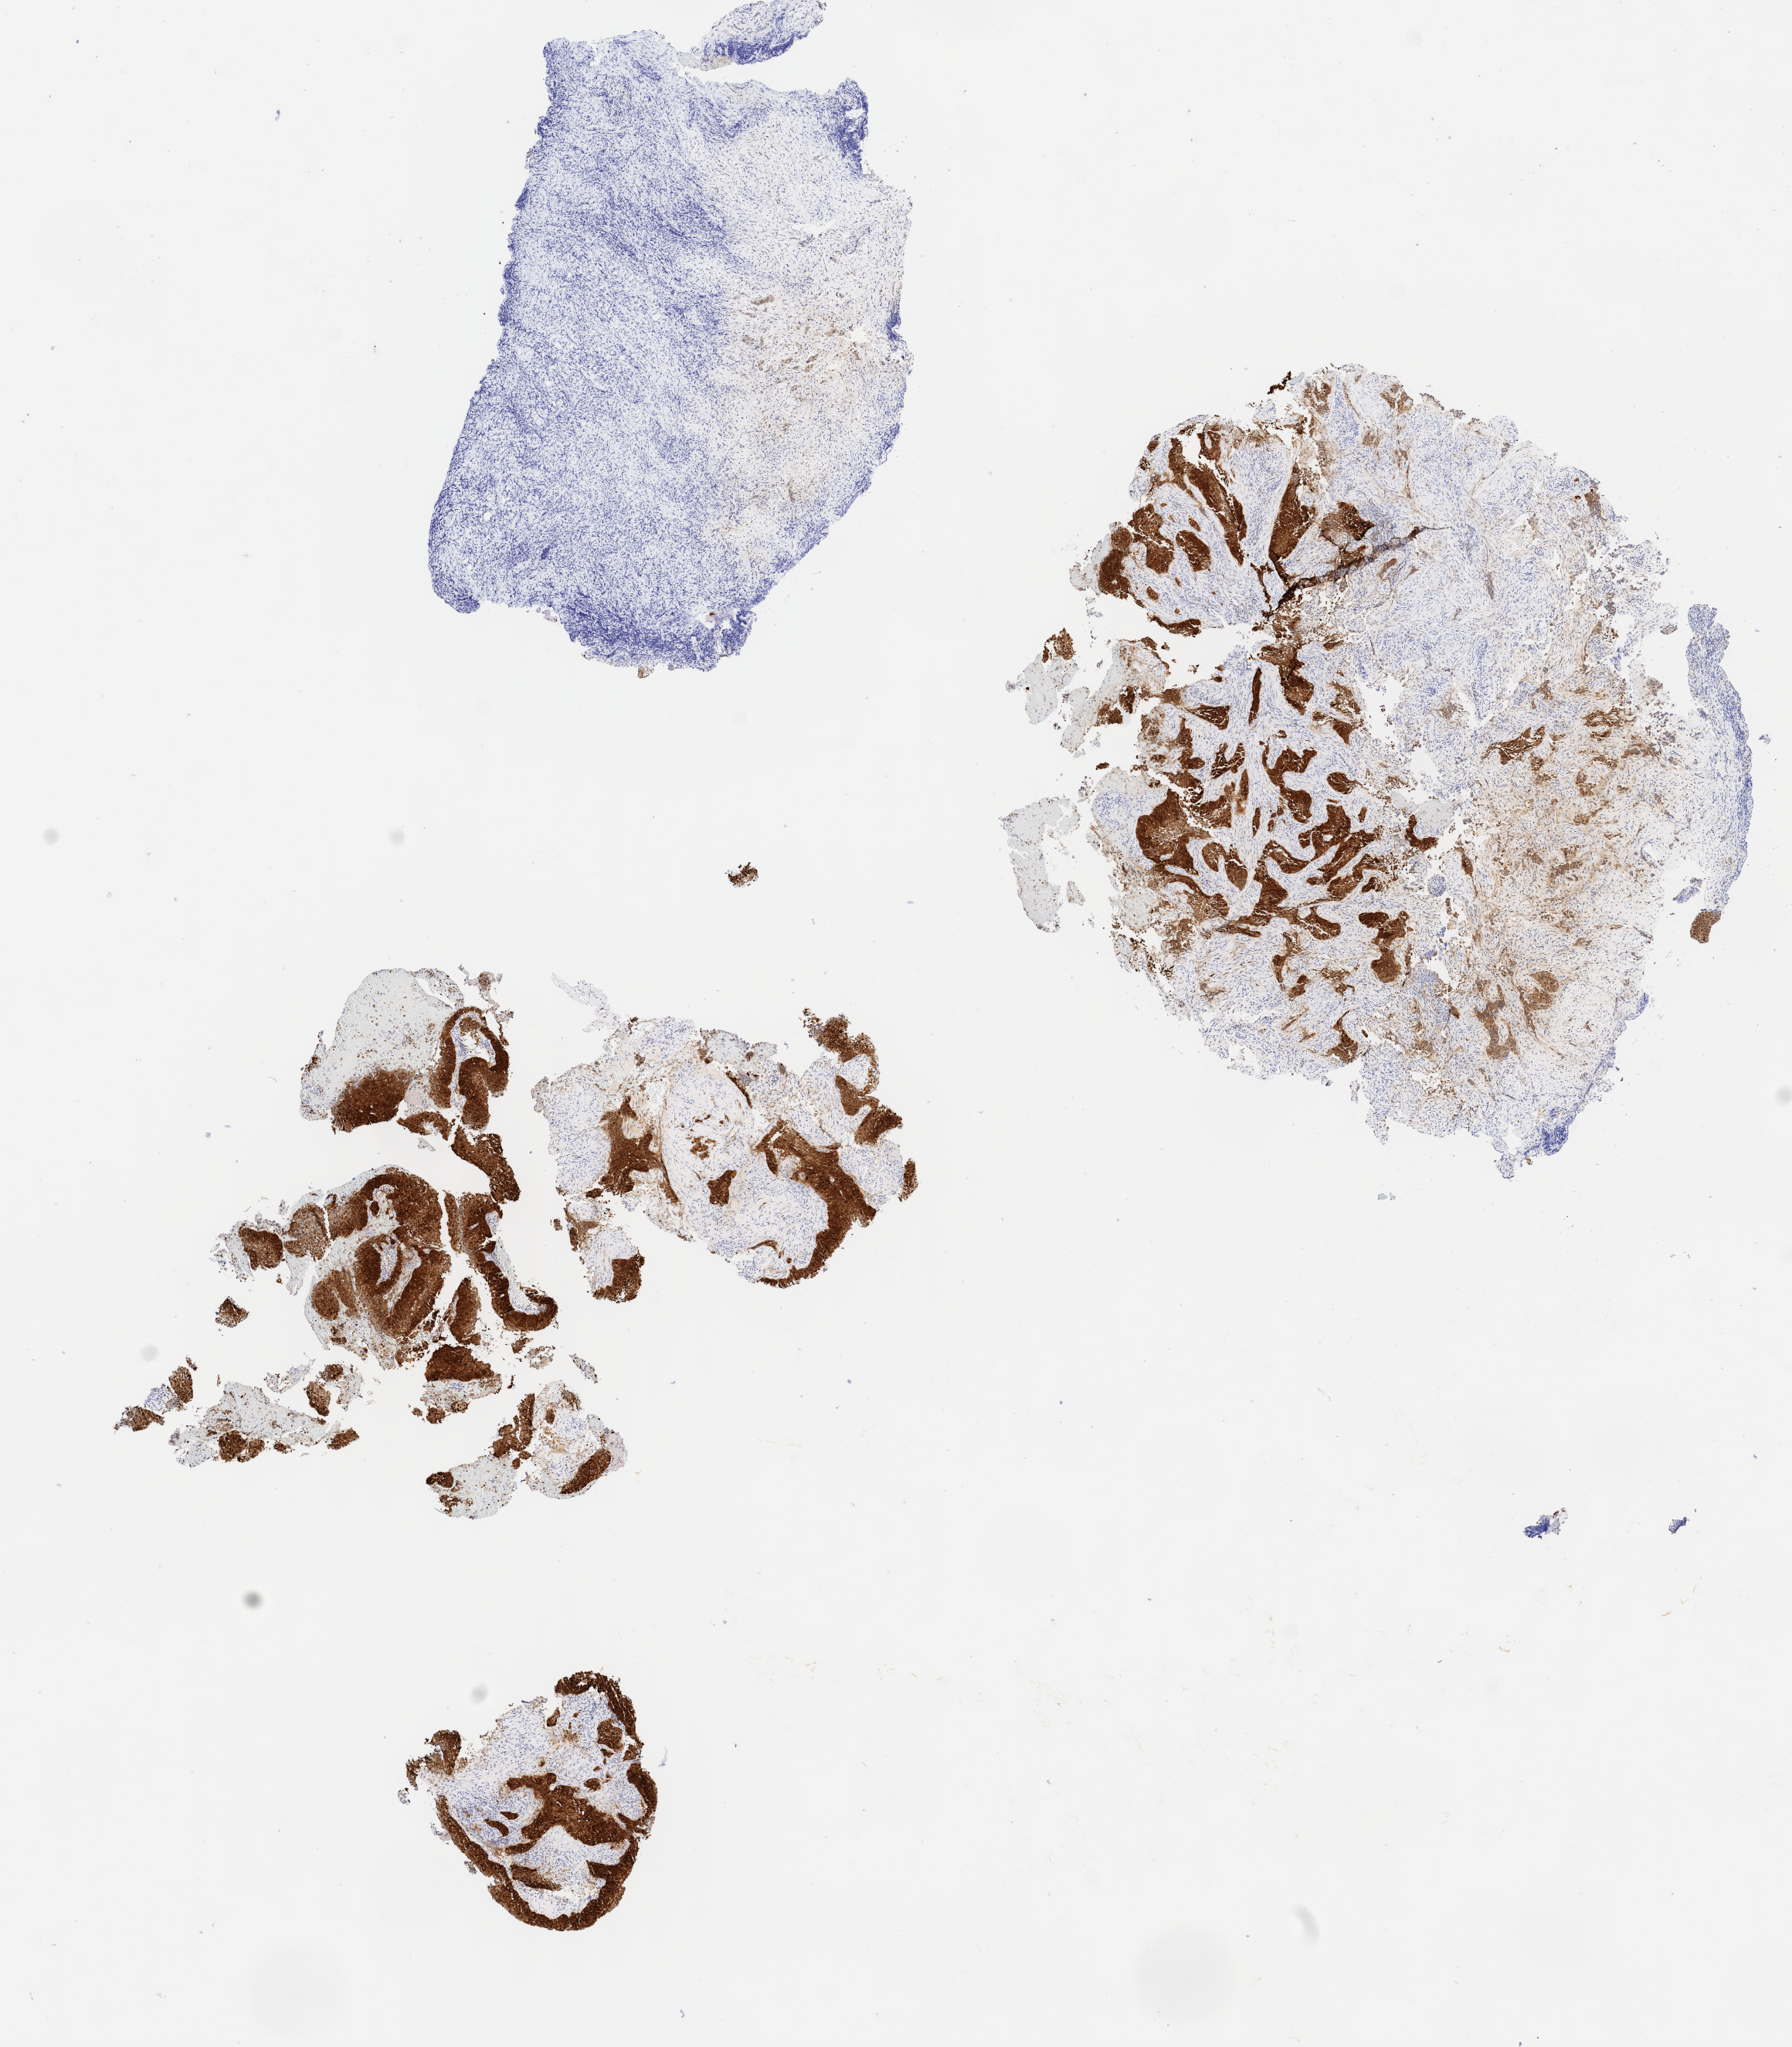
IHC for p16 (p16INK4a), whole-slide image, shown as a low-resolution overview of the whole scanned area (about 9.2 x 10.5 mm). Tumor tissue. Site: cervix. Patient: female, aged 54.
Histologic diagnosis: Squamous cell carcinoma, large cell, nonkeratinizing, NOS.